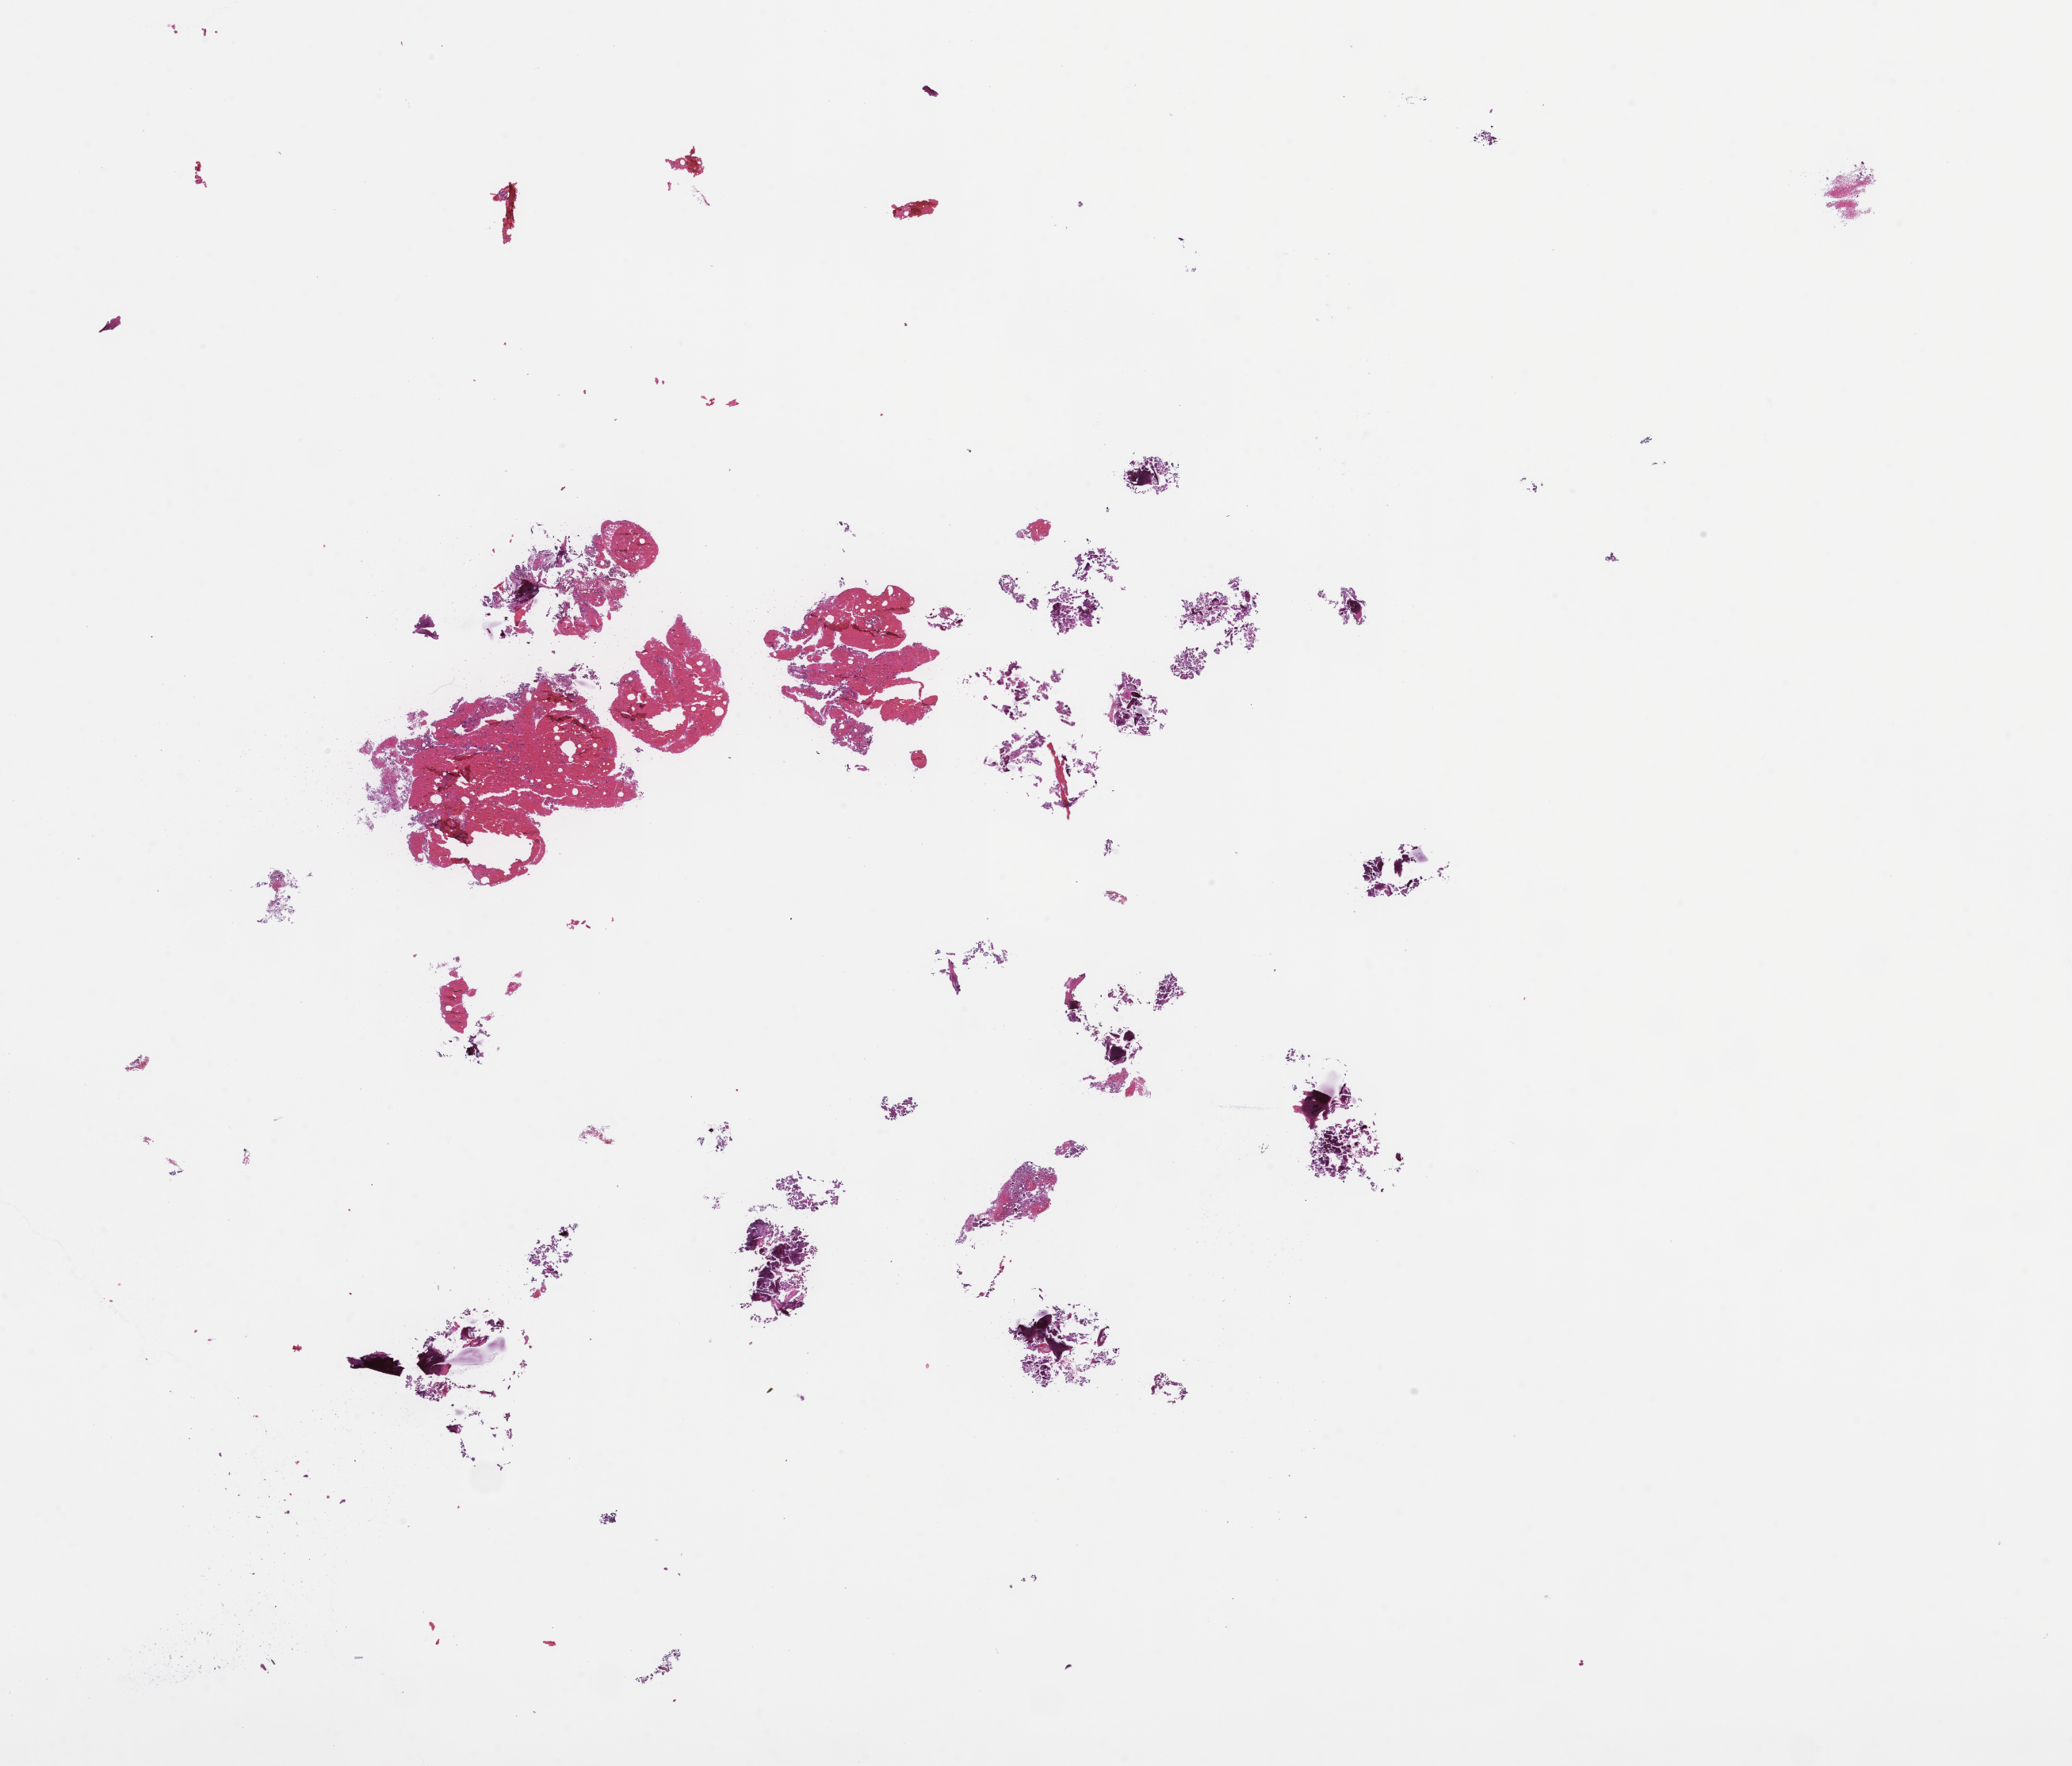
Whole-slide image, hematoxylin and eosin (H&E) stain — whole scanned area (about 21.1 x 18.0 mm) shown as a low-resolution overview; formalin-fixed, paraffin-embedded (FFPE) tissue. Patient sex: male.
This section: metastatic tumor tissue. Primary diagnosis of the patient: Prostate Carcinoma.